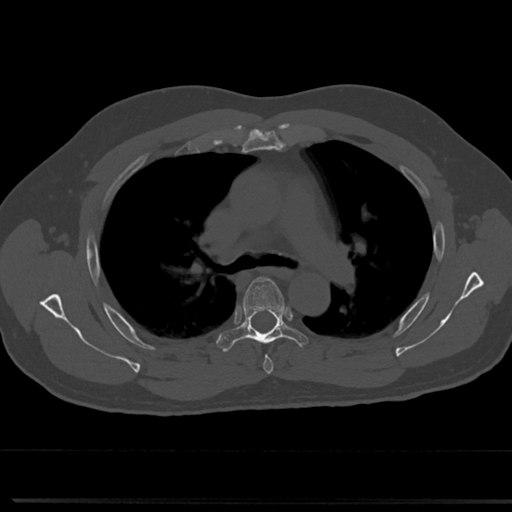
CT including the spine, one axial slice. Position 508 of 817 along the scan axis. 120 kVp. Bone window (W 1800 / L 400 HU). 0.5 mm slice thickness. 512 × 512 image matrix. Male patient, age 61 years. Case-level facts recorded for this patient, not image findings: primary cancer: prostate.
Outlined on this slice (semi-automatic segmentation, software-assisted and operator-edited):
- T4 vertebra: bounding box <261,344,273,374> (left, top, right, bottom; pixels)
- T5 vertebra: <218,276,310,352>